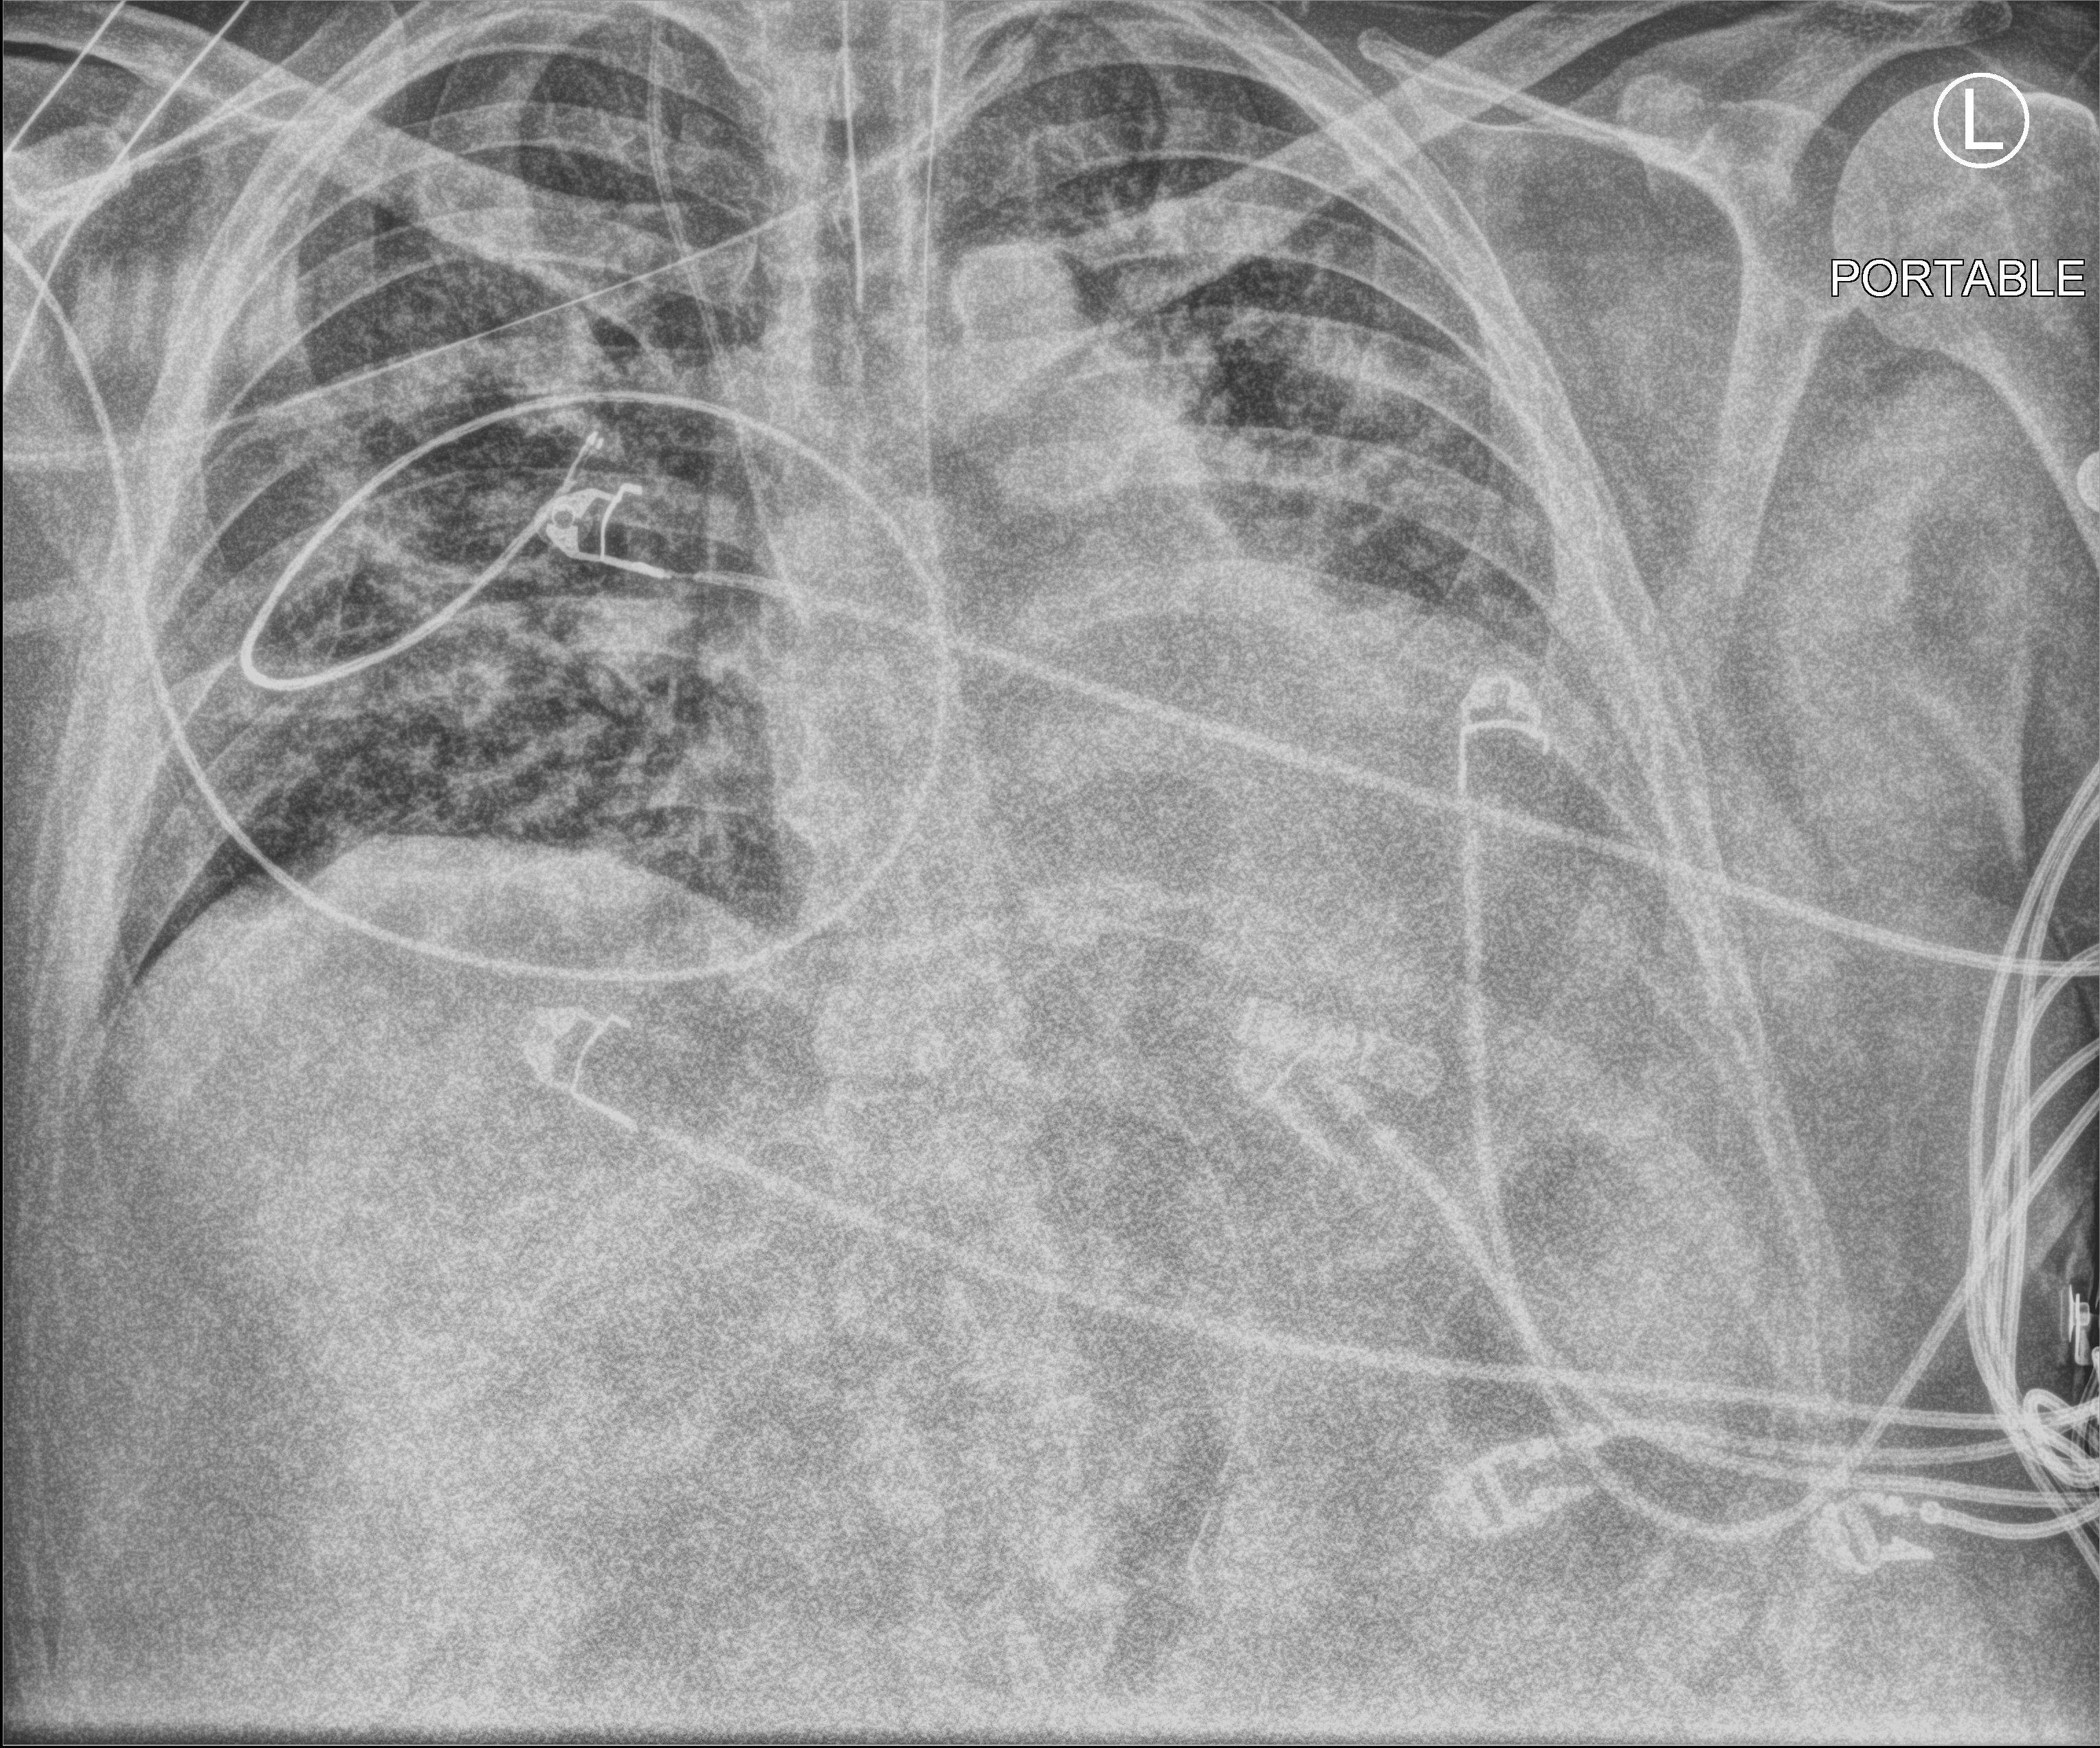
Bedside chest radiograph (computed radiography); anteroposterior (AP) projection. Patient hospitalised with COVID-19; male, aged 18–59 years.
Hospital-stay facts (about this admission, not read from this image; timing relative to this image not recorded): mechanically ventilated during this hospital stay: yes.